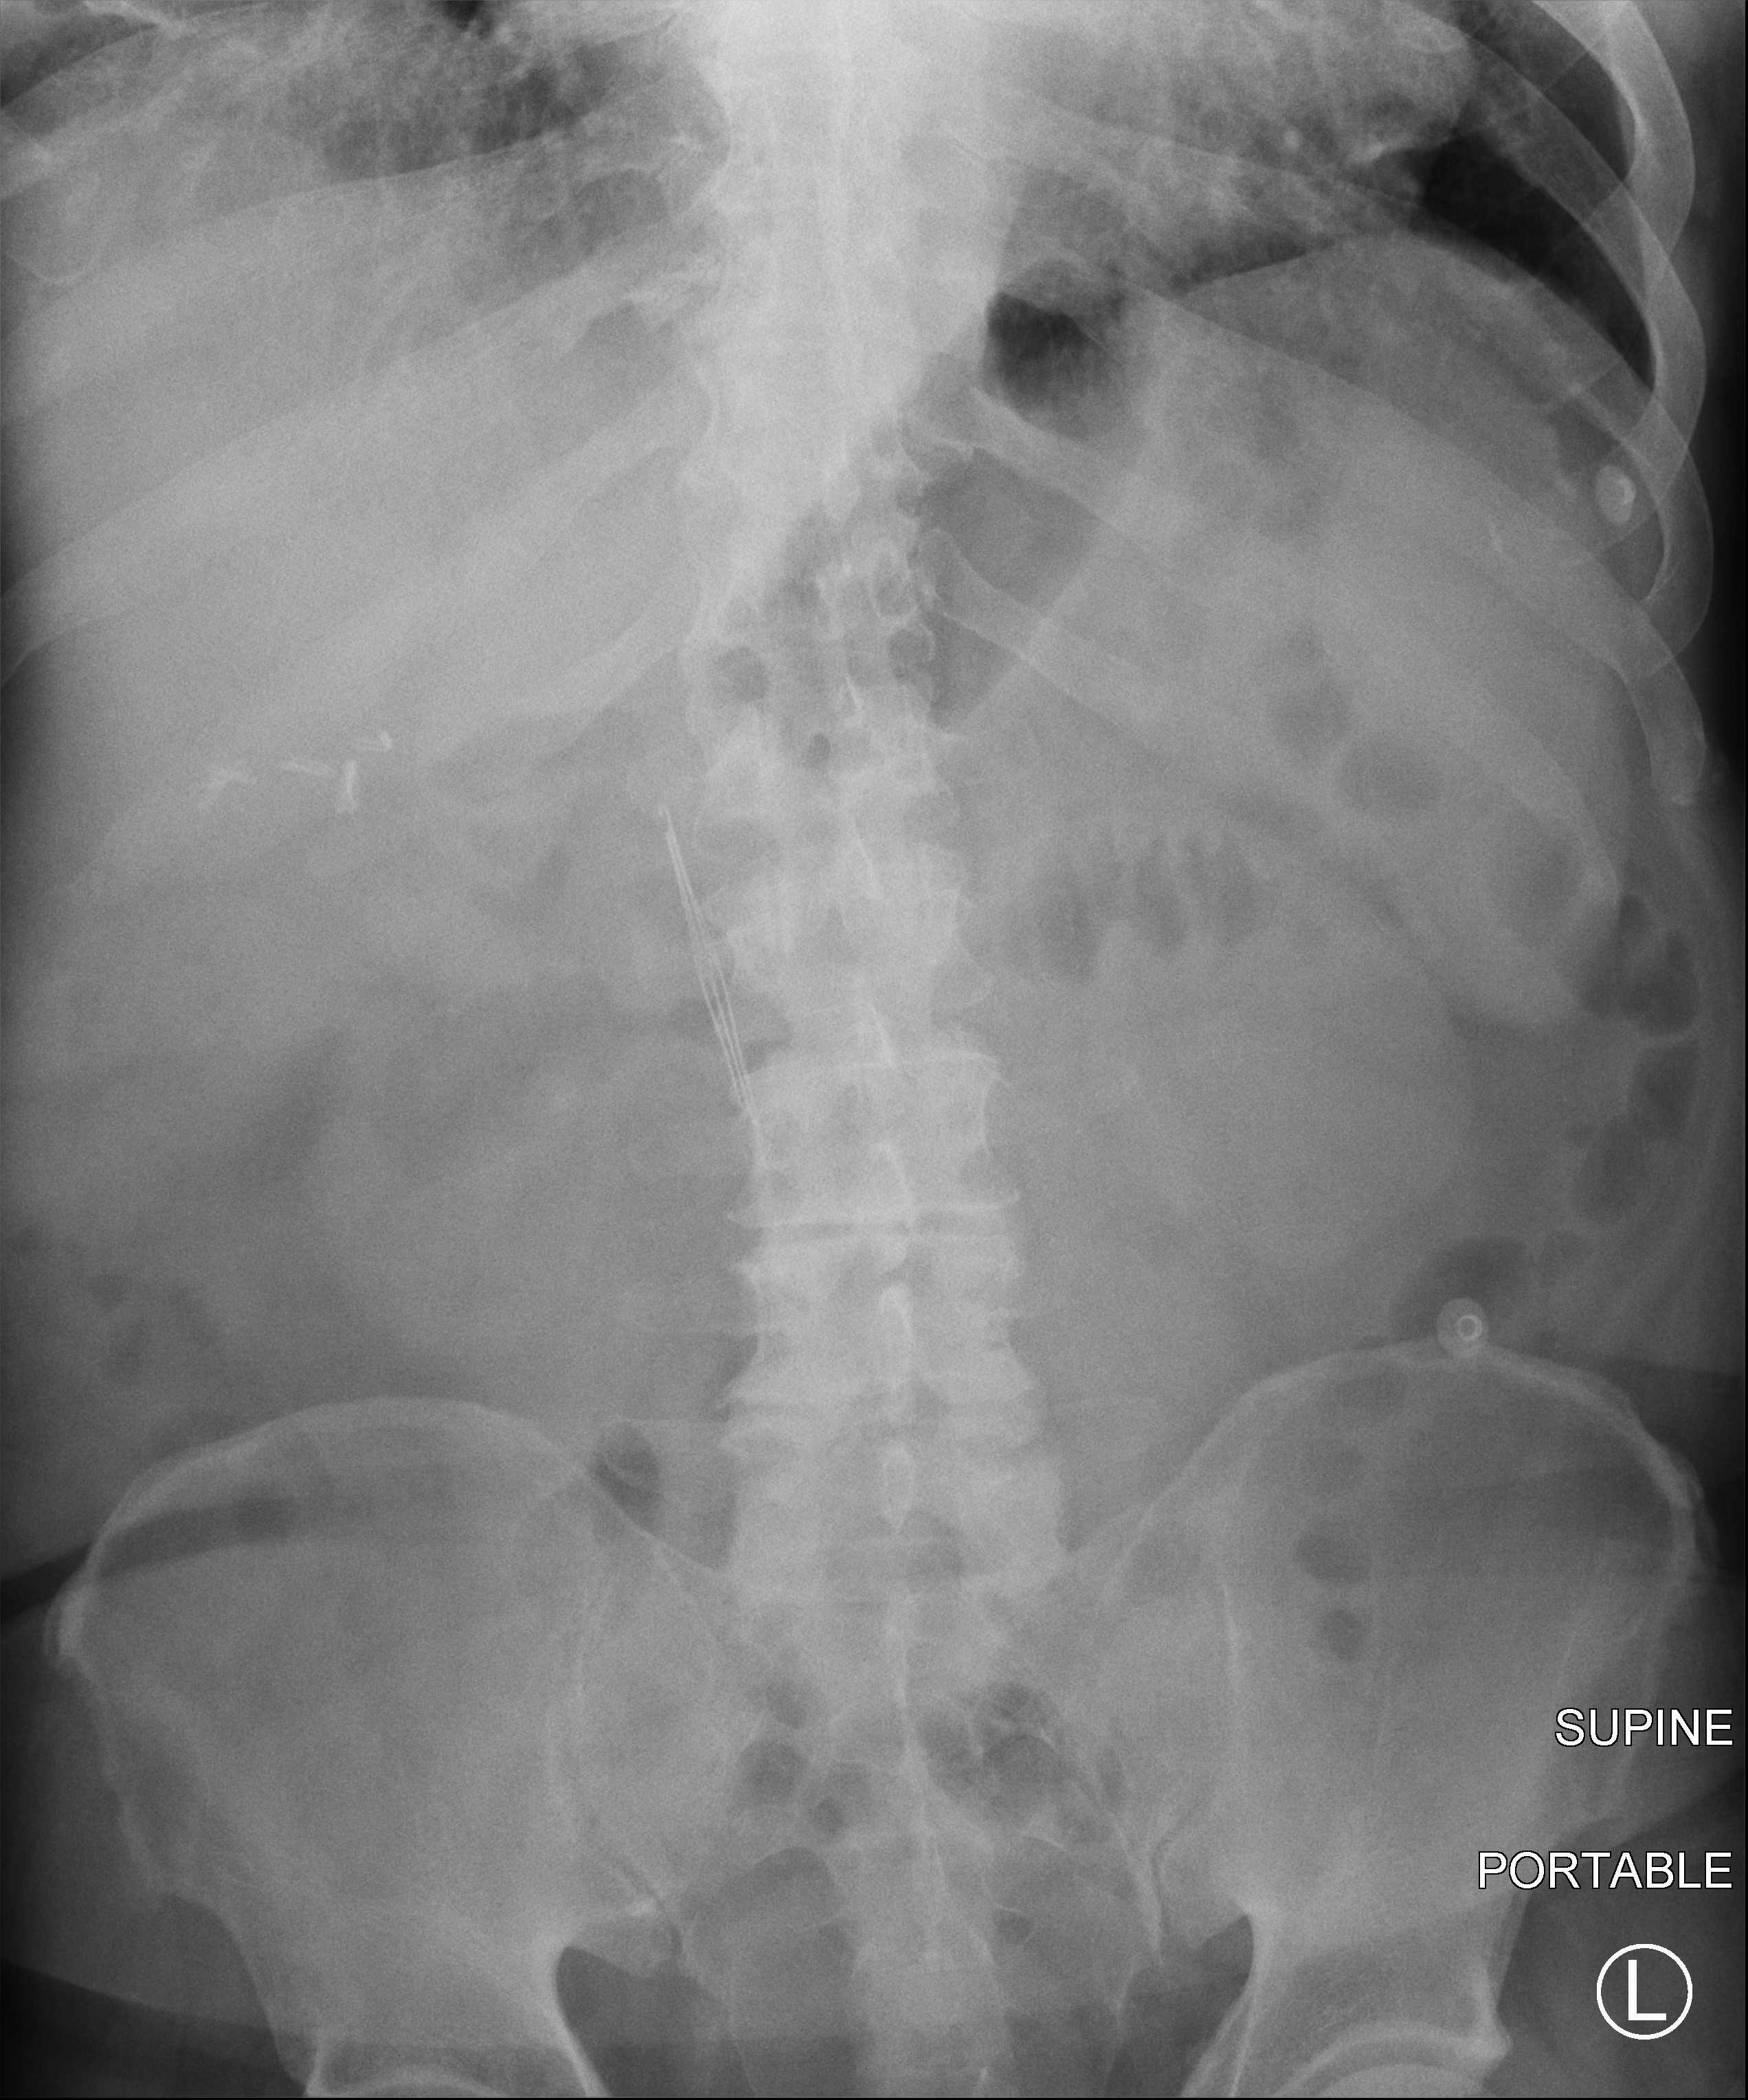
Bedside abdomen radiograph (computed radiography), anteroposterior (AP) projection. Patient hospitalised with COVID-19; male, aged 60–74 years.
Admission-level facts for this patient (not findings on this image; timing relative to this image not recorded):
- admitted to intensive care during this hospital stay: no
- mechanically ventilated during this hospital stay: no
- length of hospital stay: 4 days